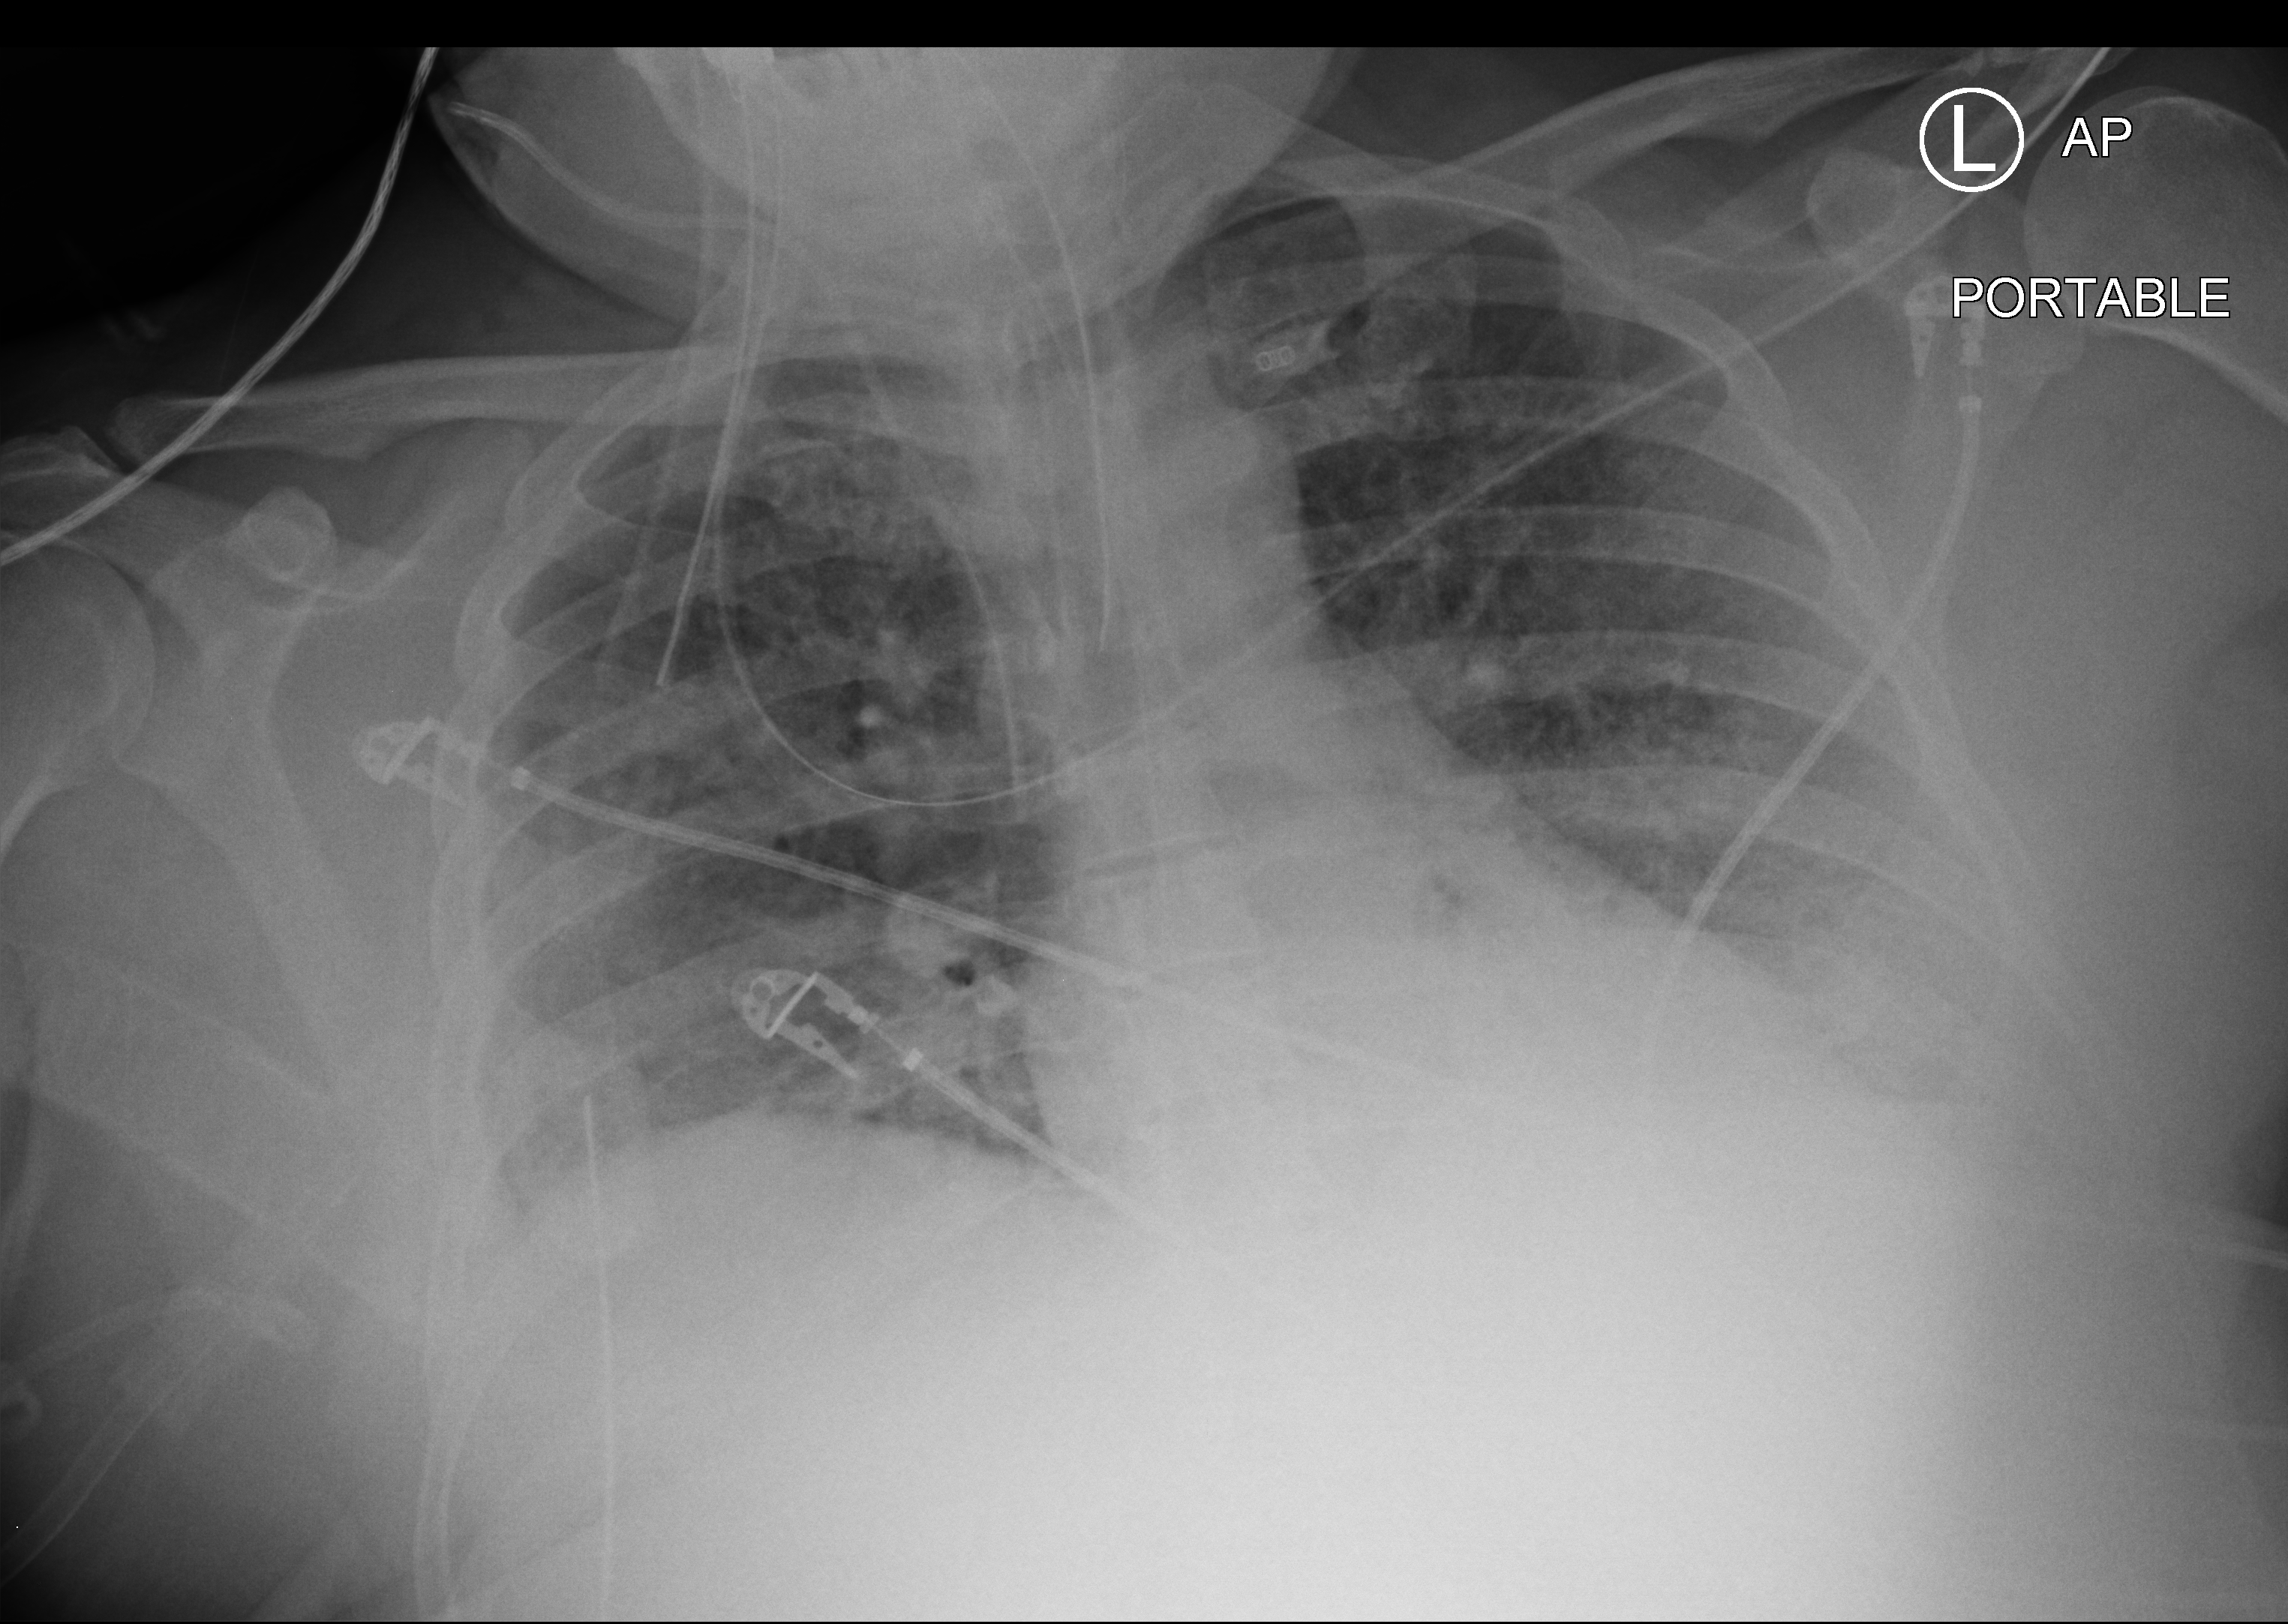
Portable chest radiograph, anteroposterior (AP) projection. Male patient hospitalised with COVID-19, age 18–59 years.
Hospital-stay facts (about this admission, not read from this image; timing relative to this image not recorded): mechanically ventilated during this hospital stay: yes.